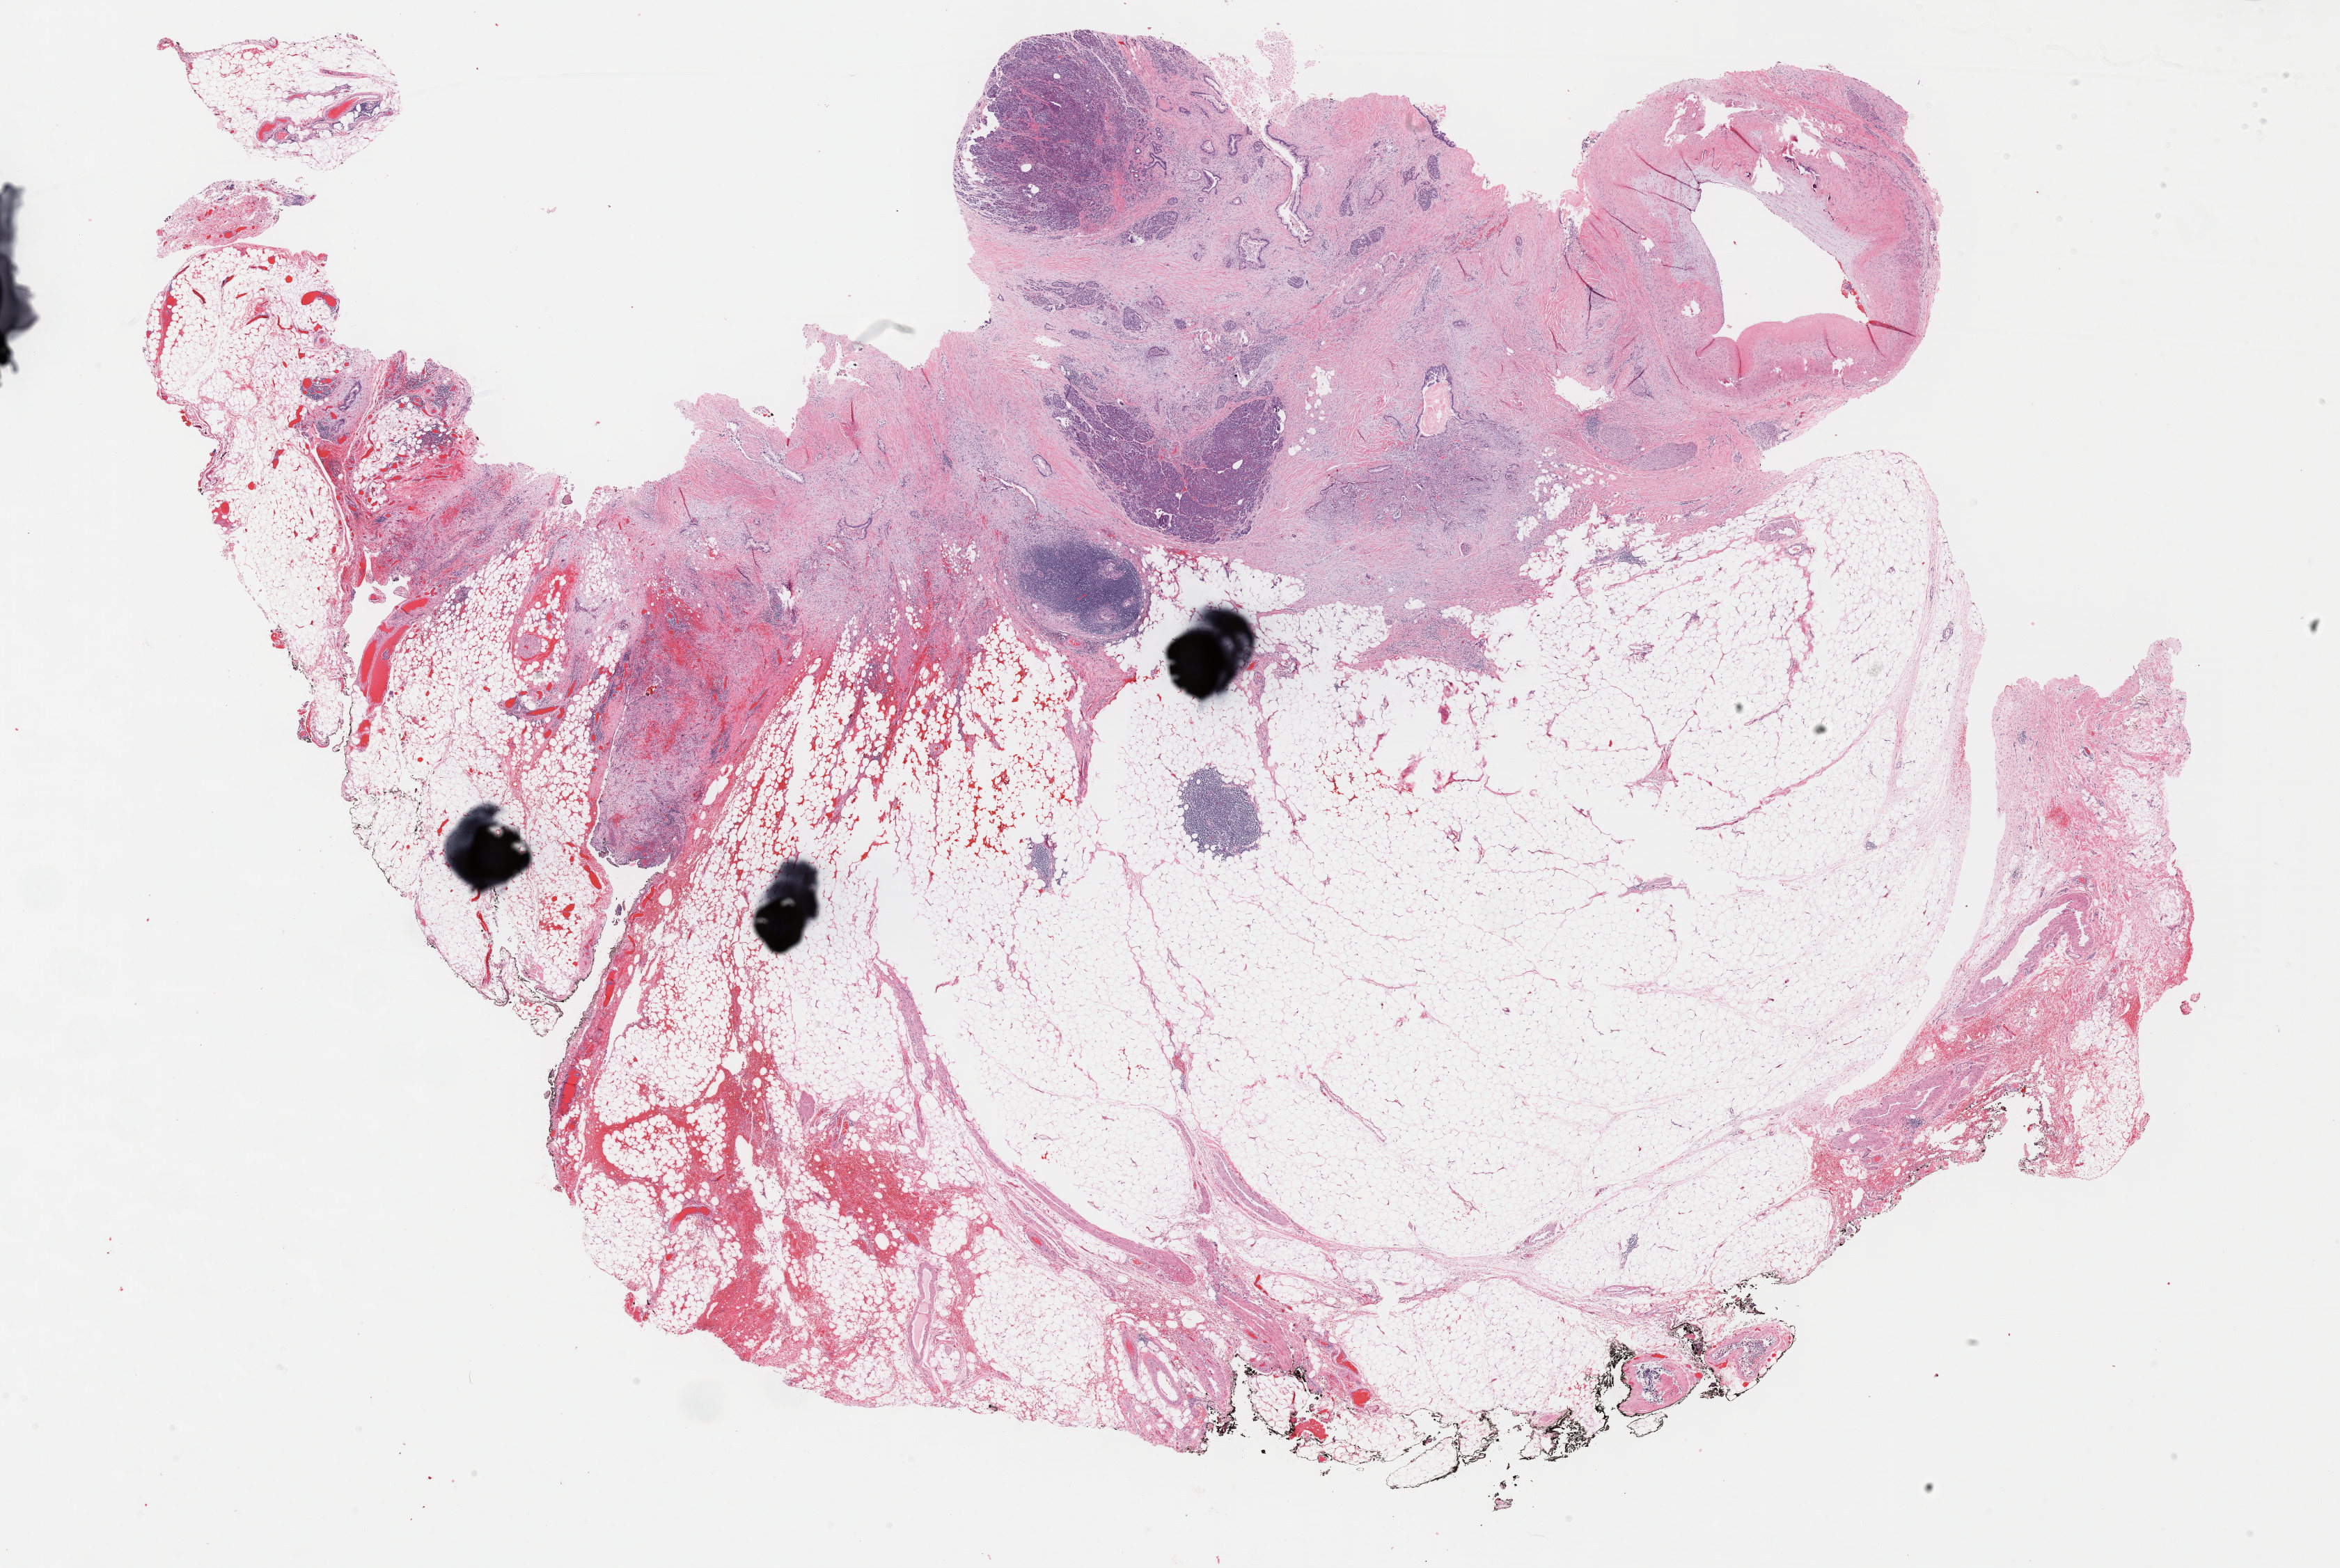
Digitized Hematoxylin and eosin (H&E) stained tissue section (whole slide), whole scanned area (about 27.2 x 18.2 mm, slide scanned at 40x) shown as a low-resolution overview, formalin-fixed paraffin-embedded (FFPE) diagnostic section, pancreas, primary tumour sample. Female patient; age at initial diagnosis 66 years. Histologic grade: G2 (moderately differentiated).
- lymph nodes positive (case pathology): 1 of 12 examined
- TNM: T3 N1 M1
- AJCC pathologic stage: IV
- histologic diagnosis: Infiltrating duct carcinoma, NOS (body of pancreas)